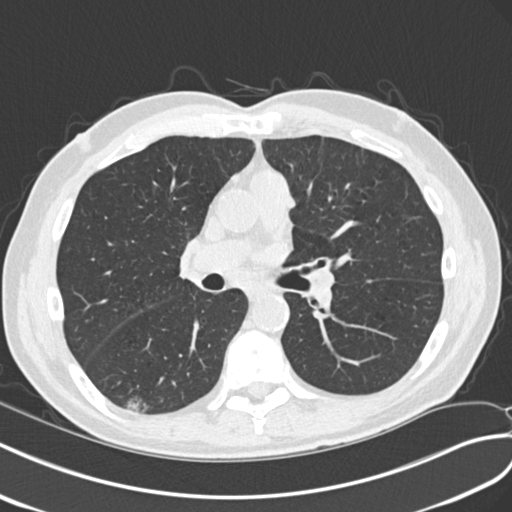
Axial slice from a low-dose chest CT screening exam. Second screening round (one year after baseline). Lung window (W 1500 / L -600 HU). 2 mm slice thickness. 512 × 512 image matrix, field of view 354 × 354 mm. Male, age 68 years at enrolment.
• Expert-annotated lung lesion, box from (x=111, y=385) to (x=161, y=422) px.
• The screening reader recorded 4 non-calcified nodules or masses ≥4 mm on this exam; which of them this box marks is not recorded.
• Later outcome: lung cancer diagnosed 653 days after this screen — non-small cell carcinoma, right lower lobe, poorly differentiated (G3), stage IA (AJCC 6th edition), 23 mm at pathology.